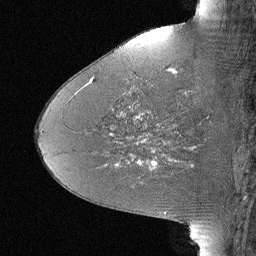
Breast MRI (dynamic contrast-enhanced), one sagittal slice; slice 27 of 64 in the series (ordered by position); dynamic contrast-enhanced study with each time point stored as its own series, time point 2 of 3 at this slice position (early post-contrast, ordered by acquisition time); 1.5 T; TE 4 ms, TR 30 ms; 2.25 mm slice thickness; 256 × 256 image matrix, field of view 180 × 180 mm. Patient: female, 46 years. From the clinical record (not read from this slice): setting: breast cancer imaged before/during neoadjuvant chemotherapy; receptor status: HR-positive, HER2-negative.
Outlined on this slice (semi-automatically segmented with operator editing):
- analysis volume of interest (the breast-tissue region the enhancement analysis was run in; not a lesion): bounding box [x1, y1, x2, y2] px = [106, 43, 184, 119]
- tumour enhancement mask (voxels above the 90 % enhancement threshold inside the analysis volume of interest): [137, 70, 177, 118]